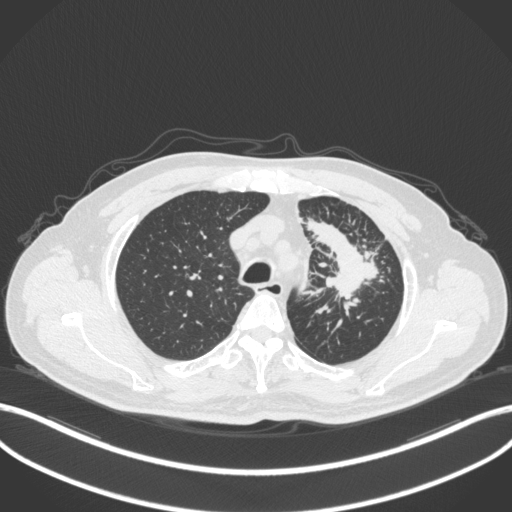
Chest CT, one axial slice; slice 278 of 386 in the series (ordered by position); reconstruction kernel B31f; 120 kVp; lung window (W 1500 / L -600 HU); 512 × 512 image matrix, field of view 400 × 400 mm. Patient: male, 69 years. From the clinical record (not read from this slice): clinical TNM (as recorded): T2a N2 M0; histopathological grade: G2-3.
Annotated regions visible in this slice (bounding box drawn by a radiologist):
- lung tumour (recorded histology: adenocarcinoma): box from (x=304, y=217) to (x=385, y=303) px